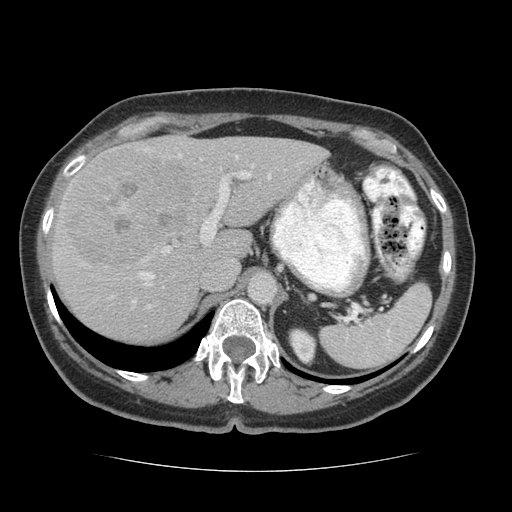
Contrast-enhanced abdominal CT (liver protocol), one axial slice; reconstruction kernel STANDARD; soft-tissue window (W 400 / L 40 HU); 512 × 512 image matrix, field of view 360 × 360 mm. Case-level facts recorded for this patient, not image findings: diagnosis: hepatocellular carcinoma (patient treated with transarterial chemoembolisation; whether this scan precedes or follows treatment is not stated here); TNM stage (as recorded): Stage-I; Child-Pugh class: A; tumour differentiation: moderately differentiated; tumour nodularity: uninodular.
Annotated regions visible in this slice (semi-automatically segmented with operator editing):
- liver parenchyma outside the tumour (the mass and vessels are separate outlines, so this box may not span the whole liver): bounding box [x1, y1, x2, y2] px = [52, 134, 328, 342]
- mass: [59, 148, 193, 268]
- liver vessels: [72, 147, 271, 308]